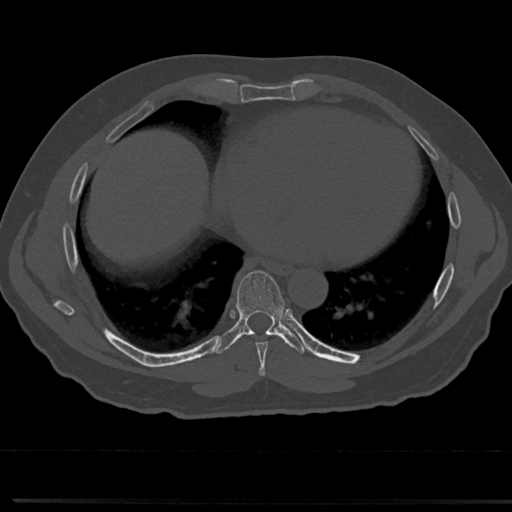
CT including the spine, one axial slice. Slice 370 of 817 in the series (ordered by position). 120 kVp. Bone window (W 1800 / L 400 HU). 0.5 mm slice thickness. 512 × 512 image matrix. Patient: male, 61 years. Case-level facts recorded for this patient, not image findings: primary cancer: prostate.
Structures marked on this image (semi-automatically segmented with operator editing):
- T7 vertebra: bounding box [x1, y1, x2, y2] px = [236, 272, 287, 358]
- T8 vertebra: [237, 324, 282, 334]